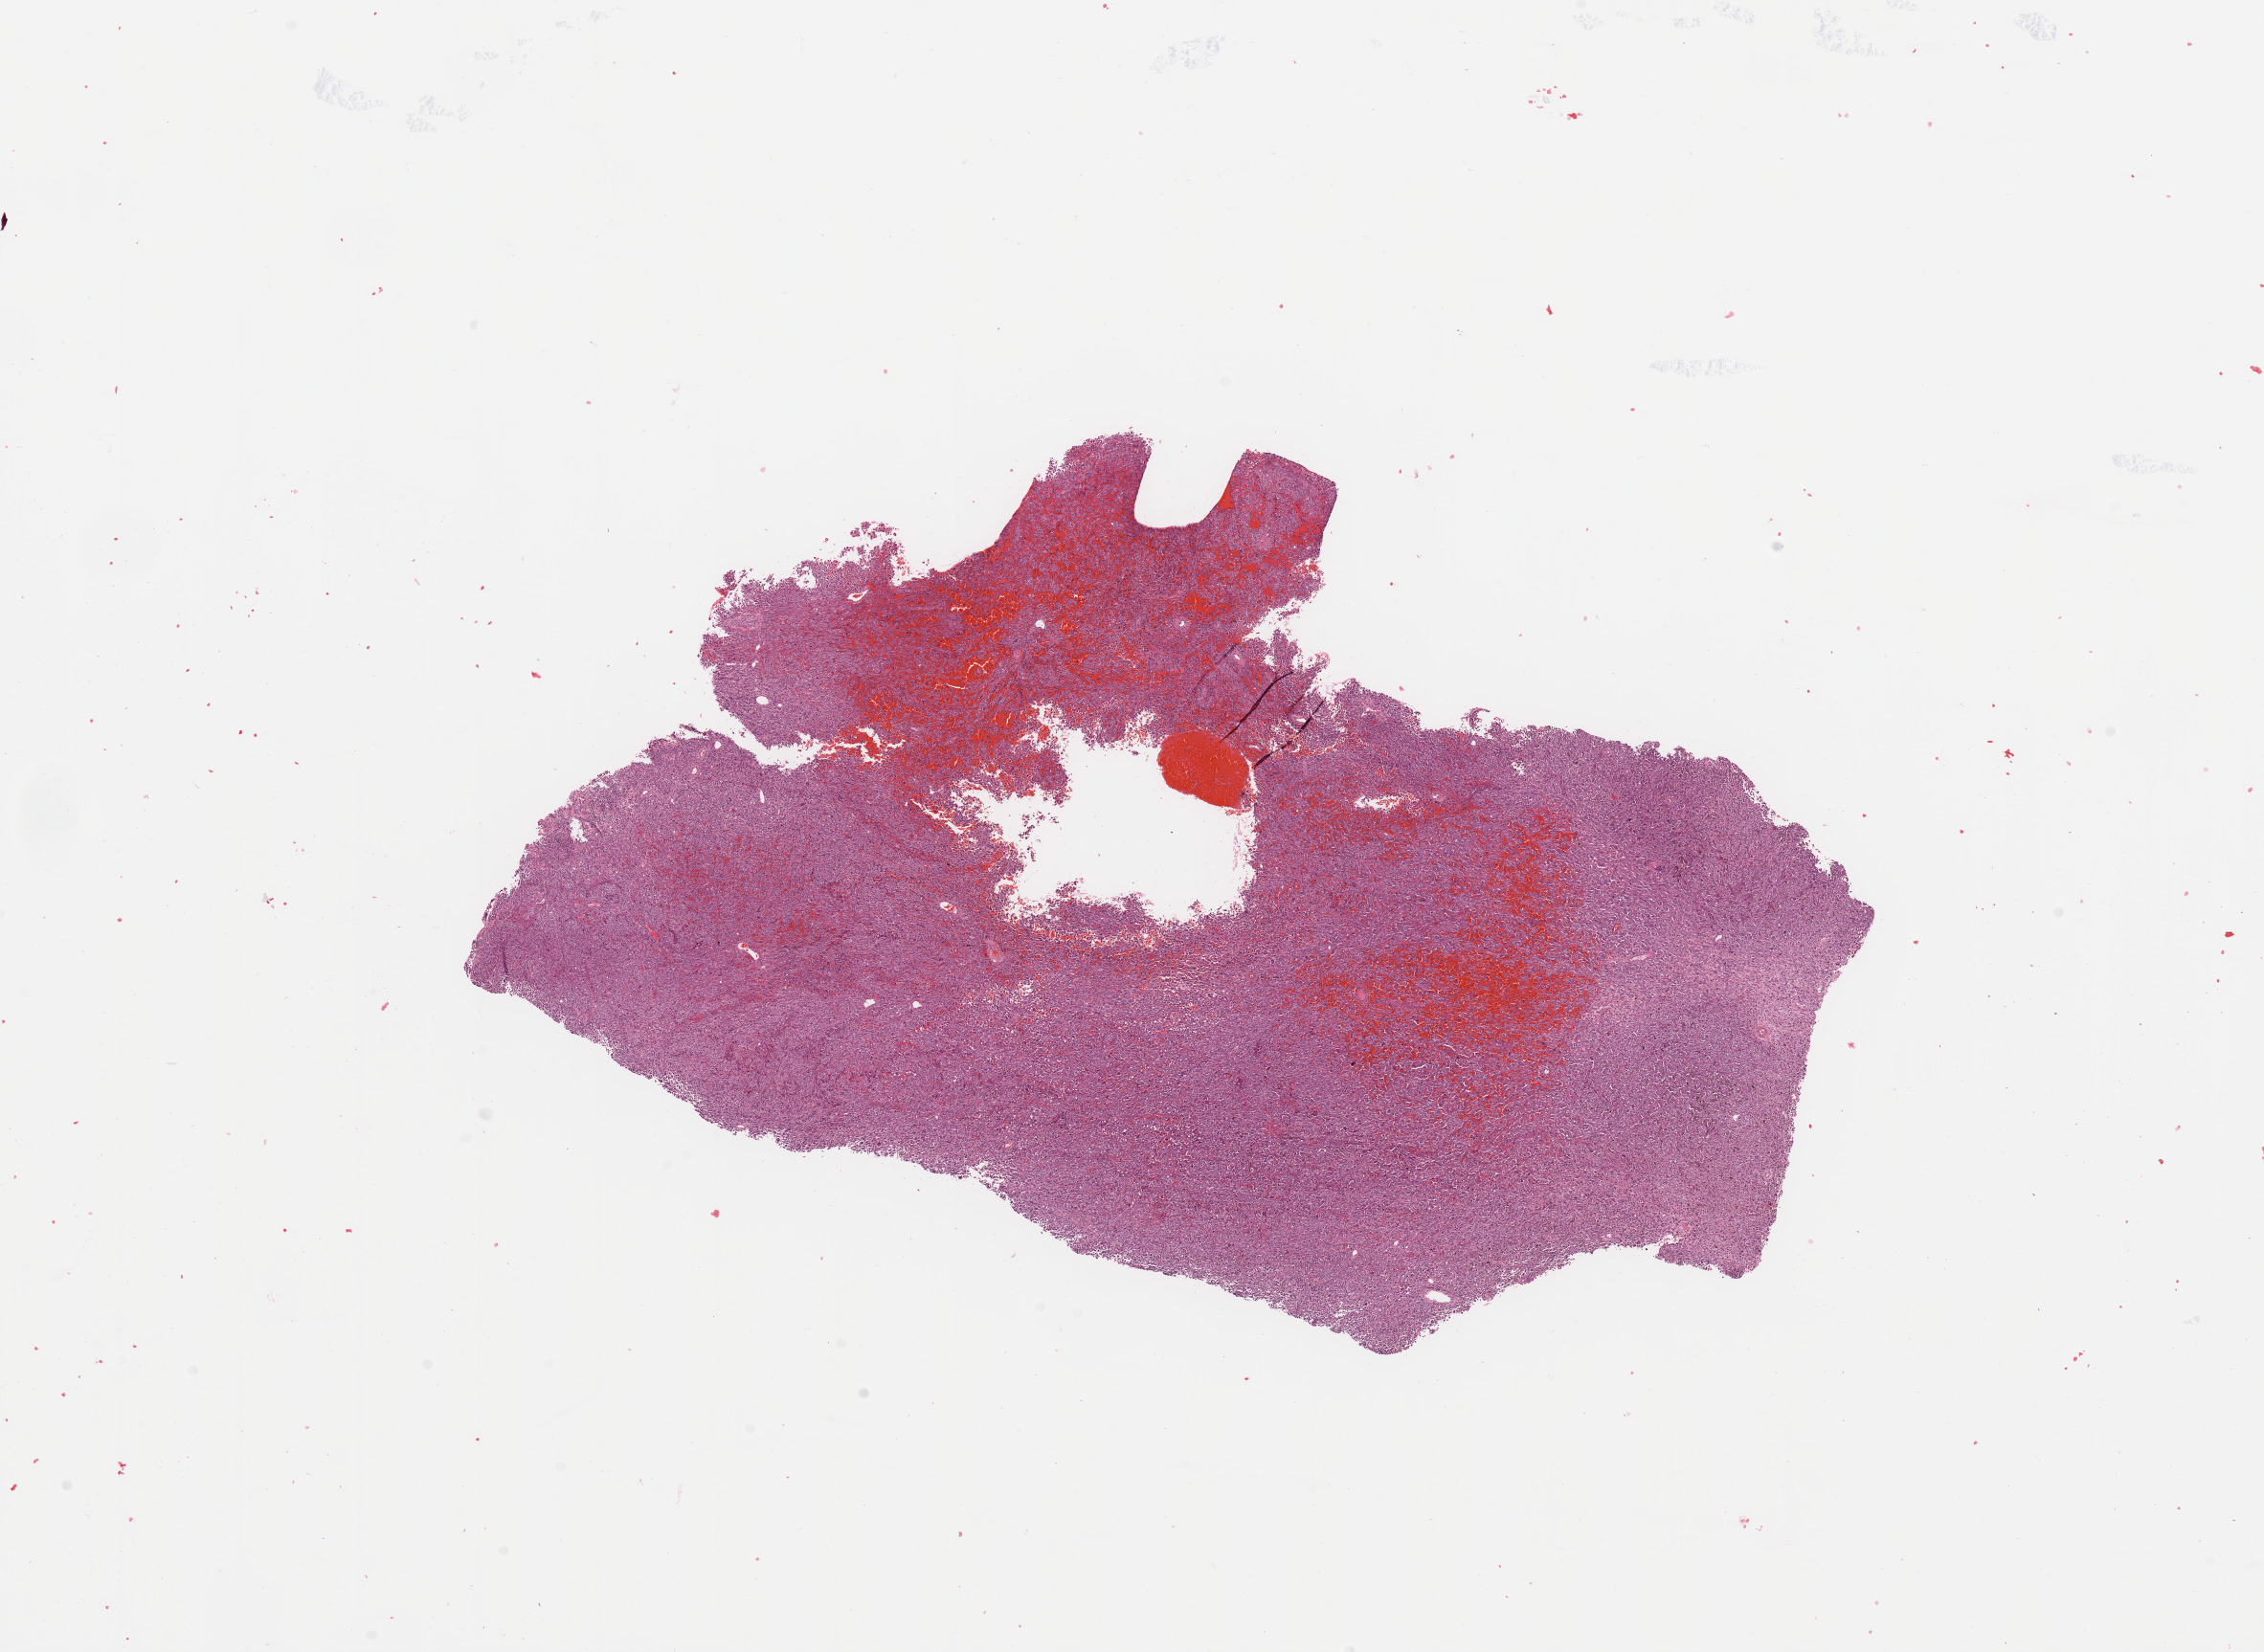
Whole-slide histology image, H&E — shown as a low-resolution overview of the whole scanned area (about 18.7 x 13.7 mm, from a 20x scan). Melanoma tumour tissue; sampled site not recorded. Patient: male, age 34 years.
AJCC pathologic stage: IIIB. Primary tumour site (as recorded): trunk. Diagnosis: Malignant melanoma, NOS.